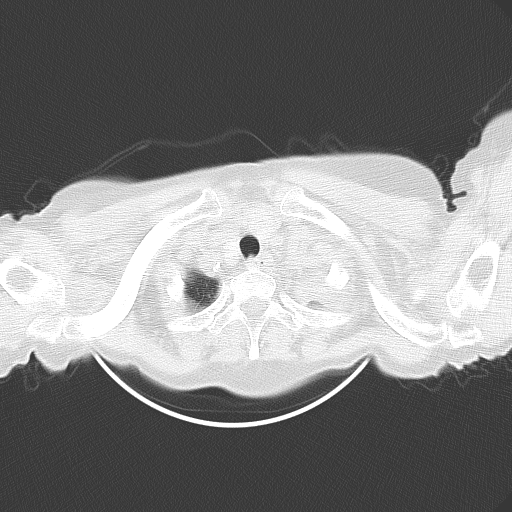
Chest CT, one axial slice; slice 50 of 54 in the series (ordered by position); 120 kVp; lung window (W 1500 / L -600 HU); 512 × 512 image matrix, field of view 353 × 353 mm. Patient: female, 71 years. Case-level facts recorded for this patient, not image findings: clinical TNM (as recorded): T3 N3 M0.
Outlined on this slice (rectangle marked by the reading radiologist):
- lung tumour (recorded histology: adenocarcinoma): bounding box [x1, y1, x2, y2] px = [282, 255, 355, 329]